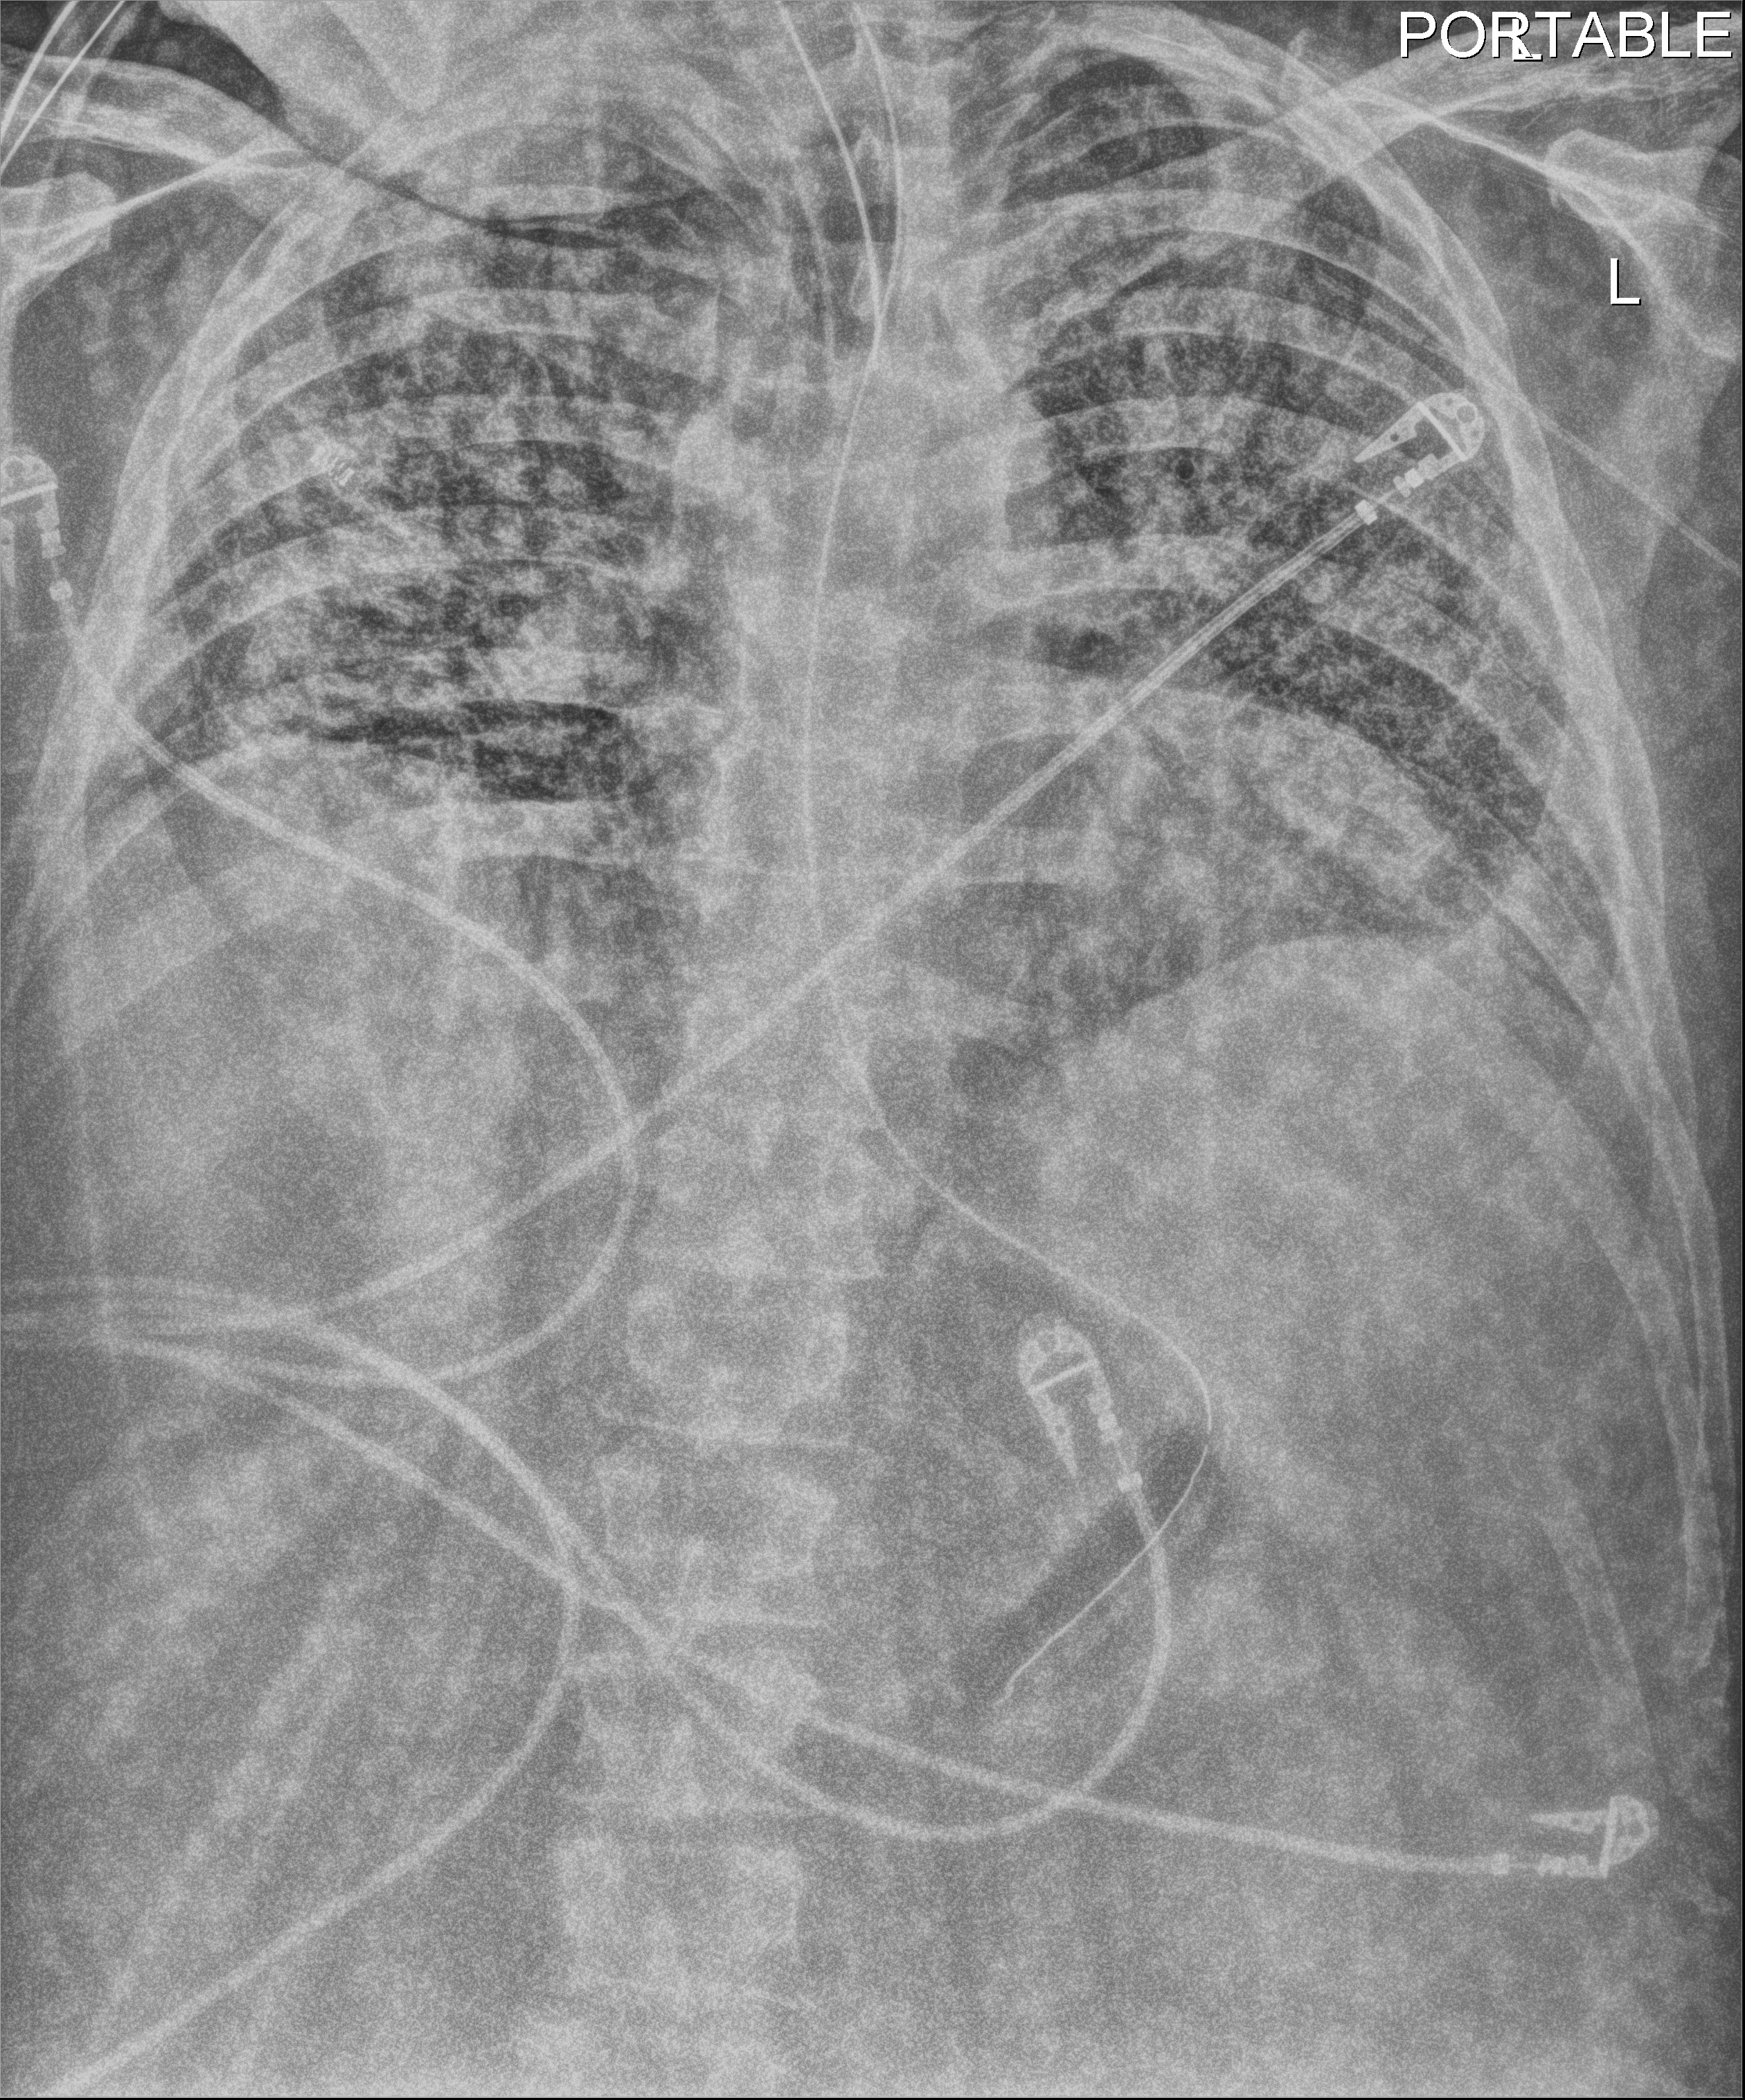
Bedside chest radiograph (digital radiography), anteroposterior (AP) projection. Patient hospitalised with COVID-19; male, aged 18–59 years.
Hospital-stay facts (about this admission, not read from this image; timing relative to this image not recorded): admitted to intensive care during this hospital stay: yes.